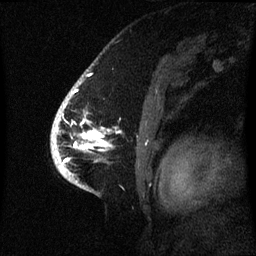
Breast MRI (dynamic contrast-enhanced), one sagittal slice. Dynamic contrast-enhanced series, image 2 of 3 at this slice position (ordered by acquisition). 1.5 T. TE 4.2 ms, TR 8.4 ms. 2.1 mm slice thickness. 256 × 256 image matrix. Female patient, age 53 years. Case-level facts recorded for this patient, not image findings: setting: breast cancer imaged before/during neoadjuvant chemotherapy; receptor status: HR-positive, HER2-negative.
Annotated regions visible in this slice (semi-automatically segmented with operator editing):
- analysis volume of interest (the breast-tissue region the enhancement analysis was run in; not a lesion): bounding box (x1, y1, x2, y2) in pixels: (52, 90, 121, 171)
- tumour enhancement mask (voxels above the 70 % enhancement threshold inside the analysis volume of interest): (55, 104, 105, 169)